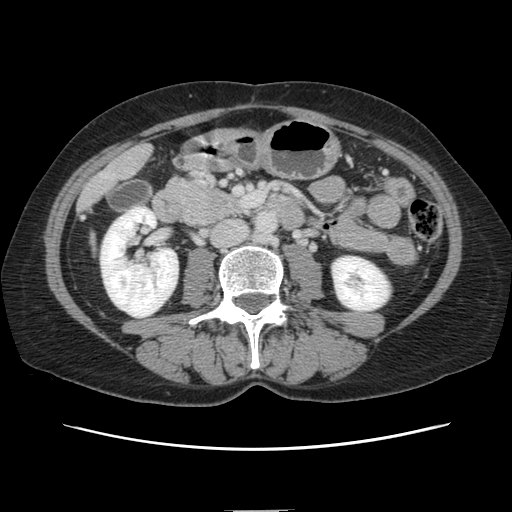
Contrast-enhanced abdominal CT, one axial slice; position 31 of 141 along the scan axis; 120 kVp; intravenous contrast given; soft-tissue window (W 400 / L 40 HU); 2.5 mm slice thickness; 512 × 512 image matrix, field of view 350 × 350 mm. Female patient, age 63 years. Case-level facts recorded for this patient, not image findings: diagnosis: colorectal cancer liver metastases, imaged before liver resection; multiple liver metastases: yes; largest metastasis: 3.2 cm; chemotherapy before resection: yes.
Annotated regions visible in this slice (expert manual segmentation):
- liver: bounding box [x1, y1, x2, y2] px = [81, 145, 151, 207]